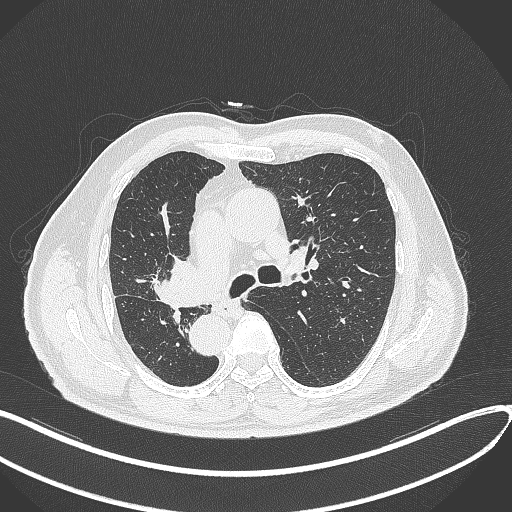
Chest CT, one axial slice; position 186 of 300 along the scan axis; lung window (W 1500 / L -600 HU); 1 mm slice thickness; 512 × 512 image matrix. Patient: male, 67 years. Case-level facts recorded for this patient, not image findings: clinical TNM (as recorded): T2a N0 M0.
Annotated regions visible in this slice (rectangle marked by the reading radiologist):
- lung tumour (recorded histology: squamous cell carcinoma): bounding box <153,253,209,311> (left, top, right, bottom; pixels)